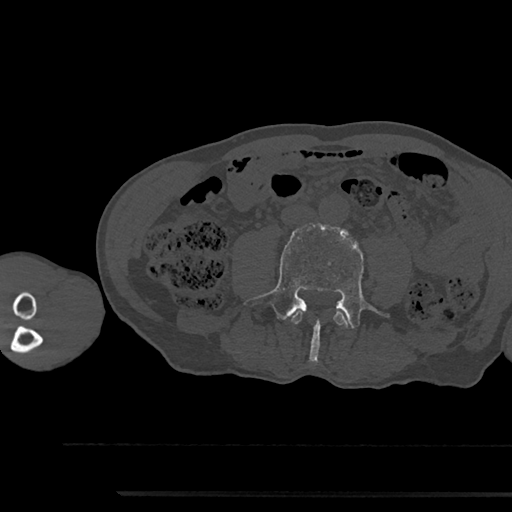
CT including the spine, one axial slice. Position 429 of 797 along the scan axis. 120 kVp. Bone window (W 1800 / L 400 HU). 0.5 mm slice thickness. 512 × 512 image matrix, field of view 367 × 367 mm. Male patient, age 79 years. From the clinical record (not read from this slice): primary cancer: prostate.
Structures marked on this image (semi-automatic segmentation, software-assisted and operator-edited):
- L3 vertebra: bounding box <292,312,348,326> (left, top, right, bottom; pixels)
- L4 vertebra: <243,224,389,362>